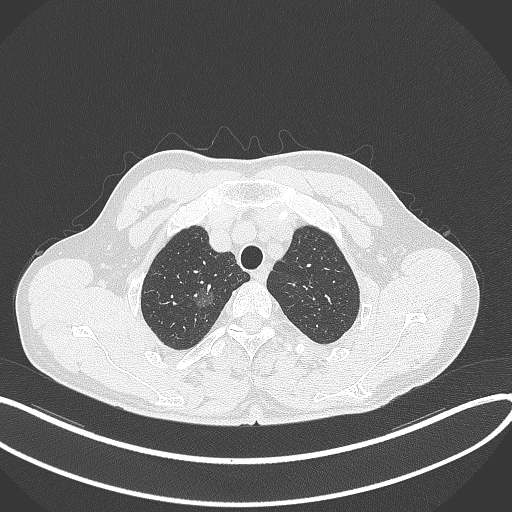
Chest CT, one axial slice. 120 kVp. Lung window (W 1500 / L -600 HU). 1 mm slice thickness. 512 × 512 image matrix, field of view 400 × 400 mm. Male patient, age 58 years. Case-level facts recorded for this patient, not image findings: clinical TNM (as recorded): T1c N0 M0; histopathological grade: G1-2.
Annotated regions visible in this slice (bounding box drawn by a radiologist):
- lung tumour (recorded histology: adenocarcinoma): bounding box <183,279,215,311> (left, top, right, bottom; pixels)